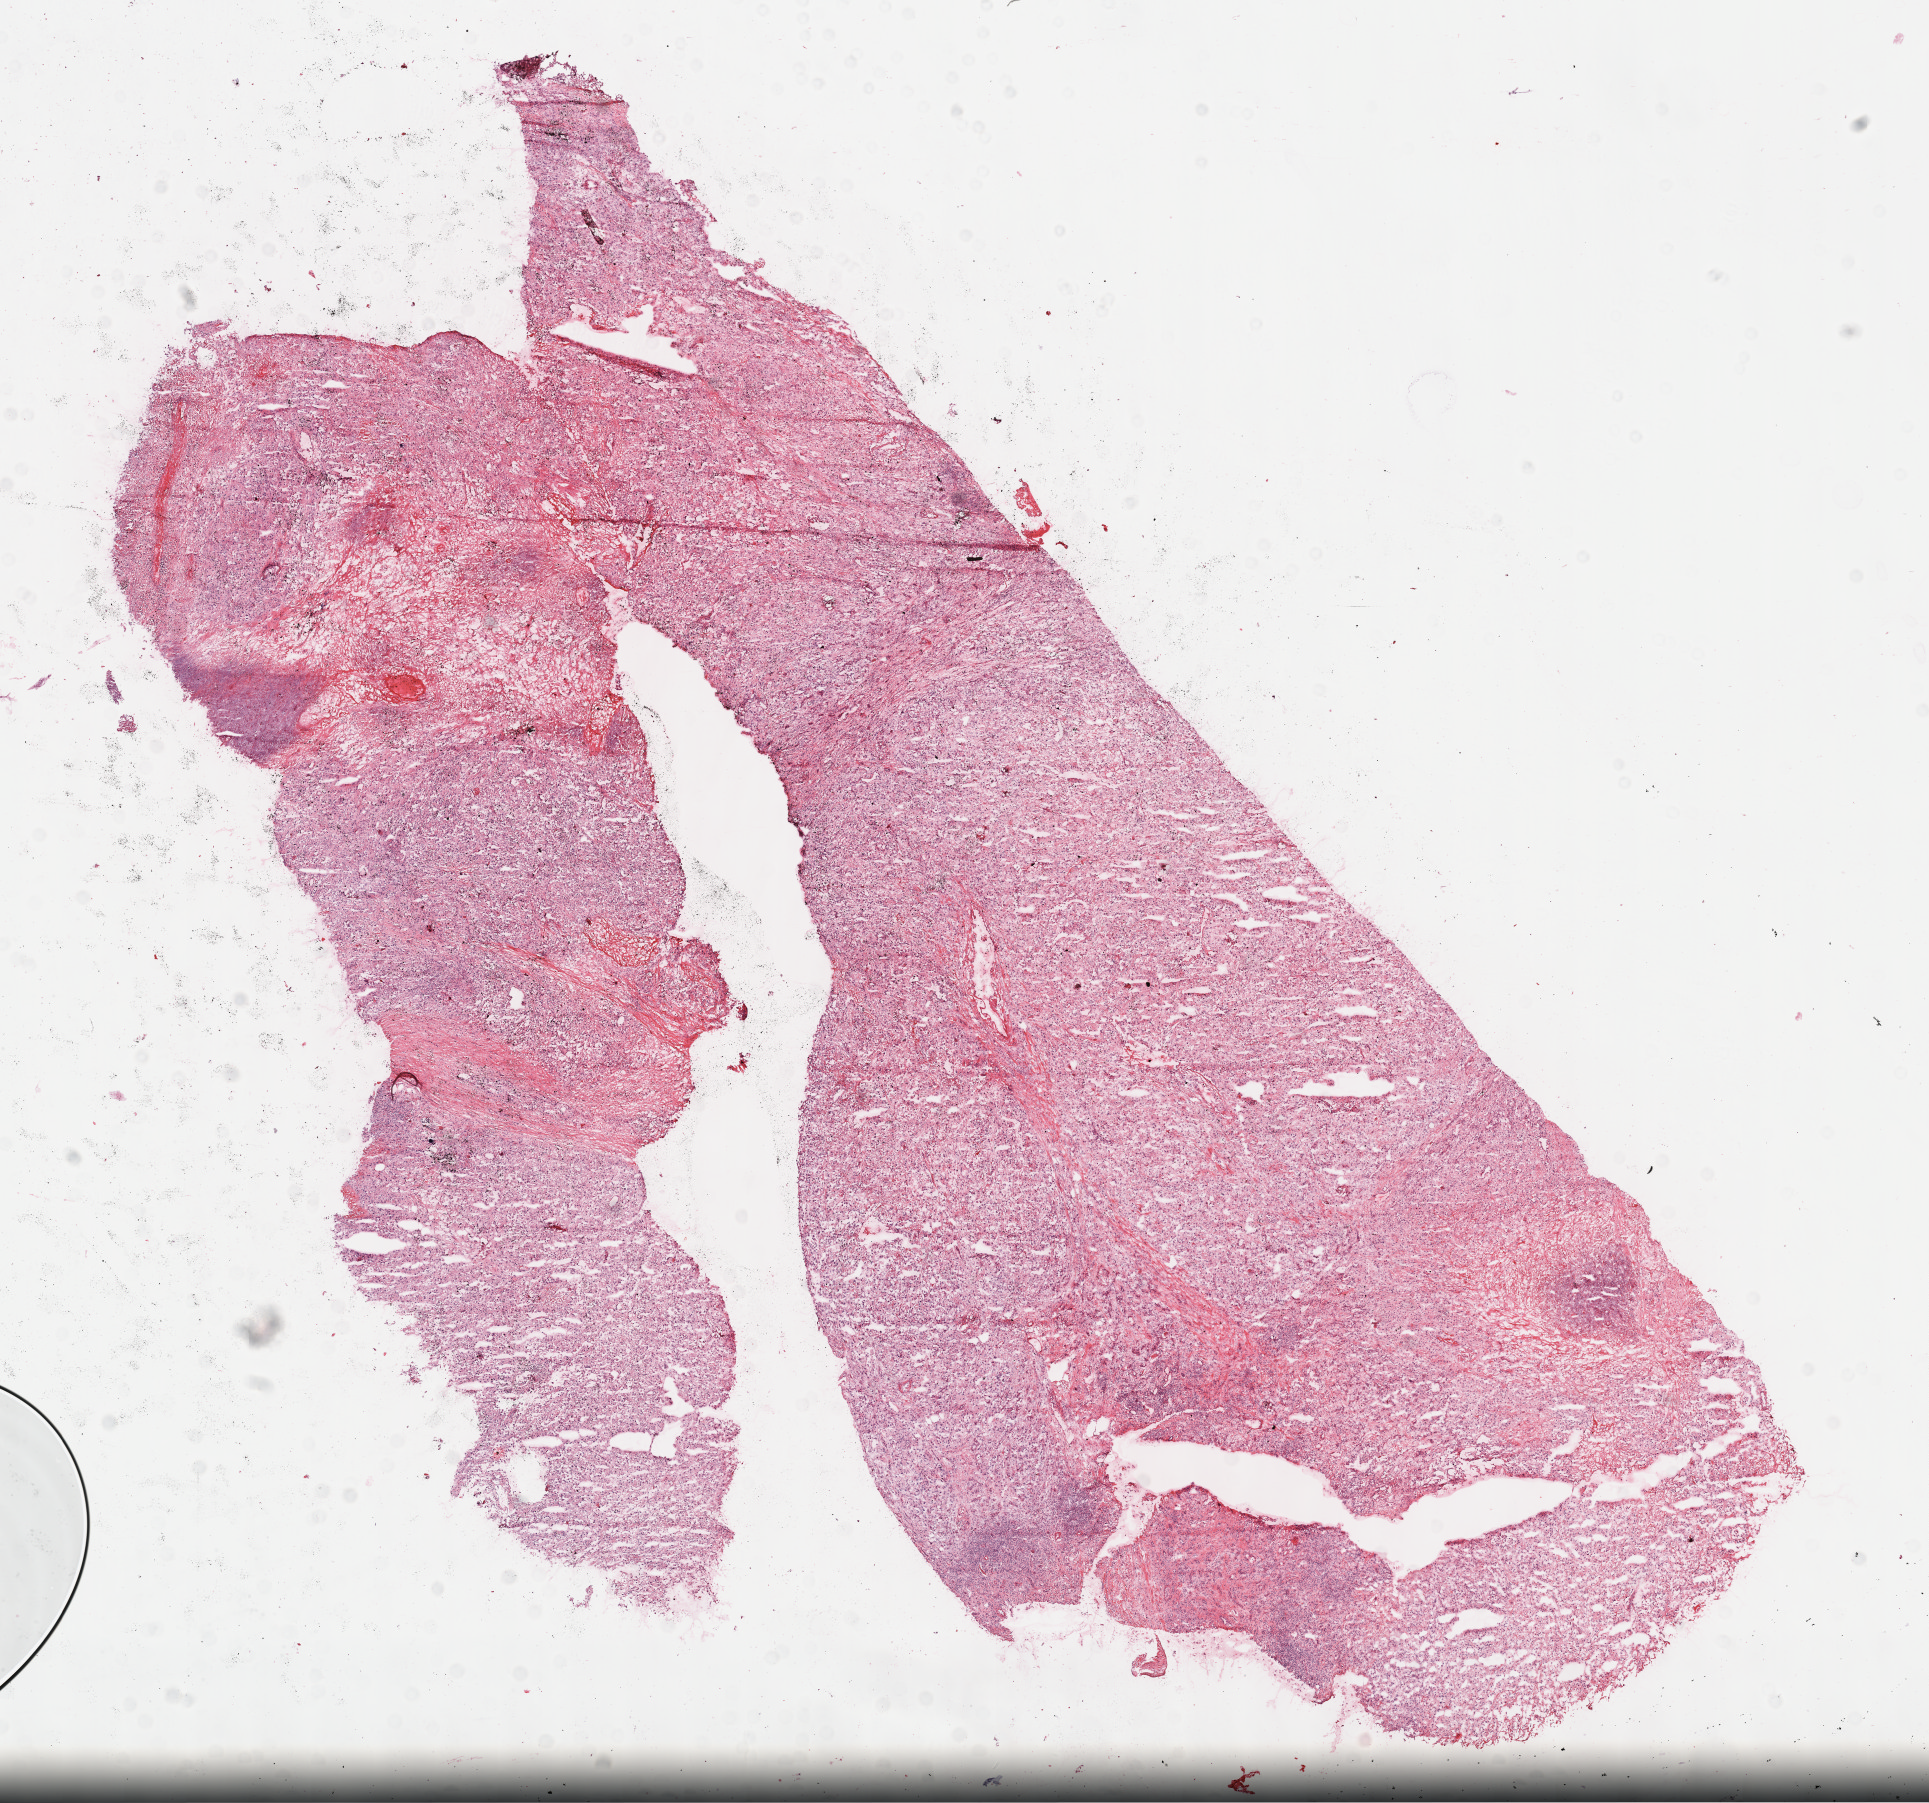
Digitized H&E-stained tissue section (whole slide) — low-resolution overview of the scanned area, about 15.6 x 14.6 mm, frozen section, kidney, primary tumour sample. Male patient; age at initial diagnosis 65 years. Pathologist review of this section (percent, as recorded): tumour cells 85%, tumour nuclei 75%.
Diagnosis: Clear cell adenocarcinoma, NOS.